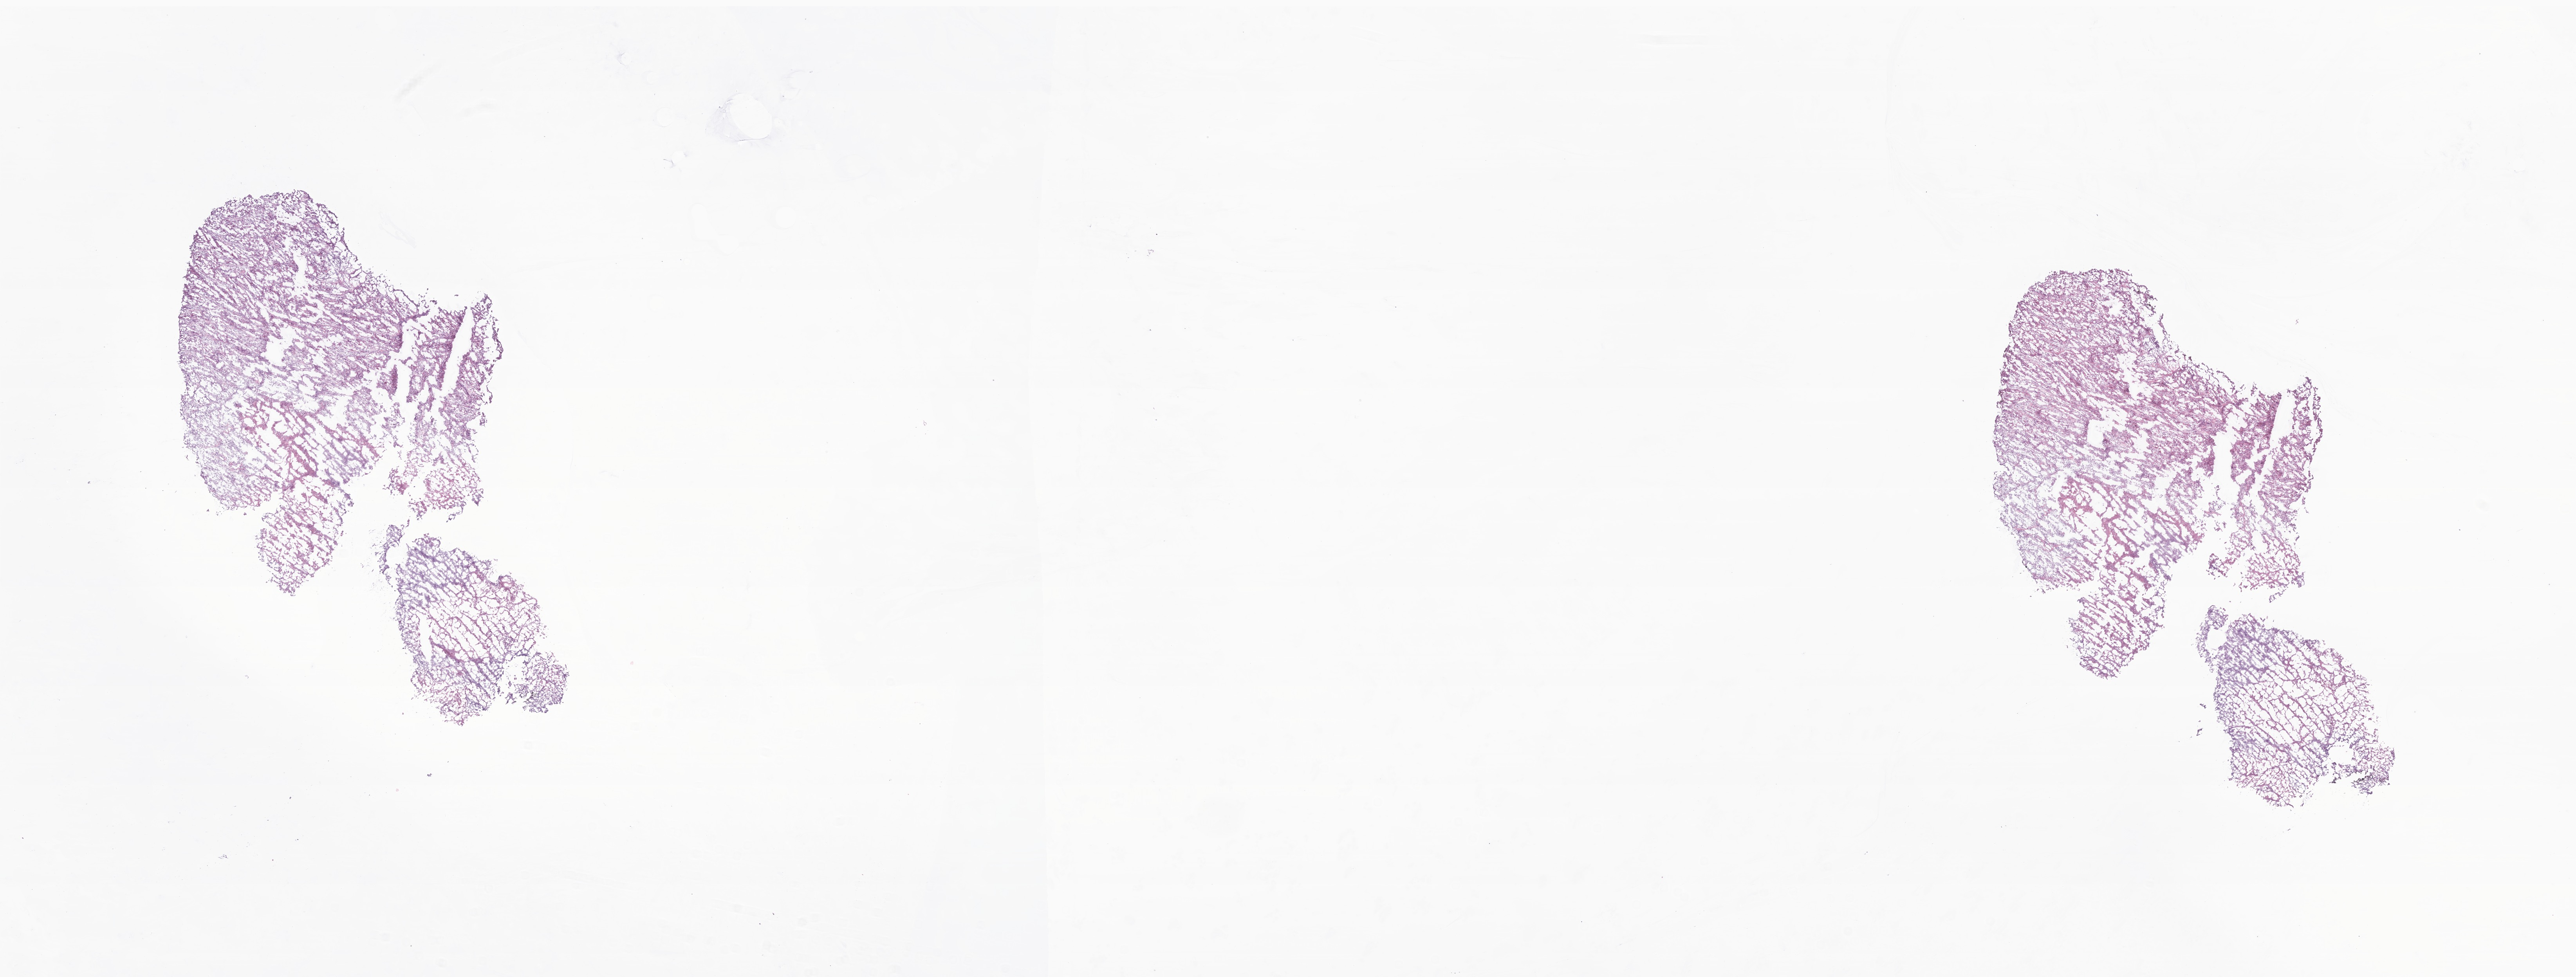
Haematoxylin and eosin whole-slide image of tumor tissue from the testis — shown as a low-resolution overview of the whole scanned area (about 27.7 x 10.5 mm), frozen section. Male patient, age 192 months (16 years).
Recorded diagnosis: Embryonal rhabdomyosarcoma, NOS.